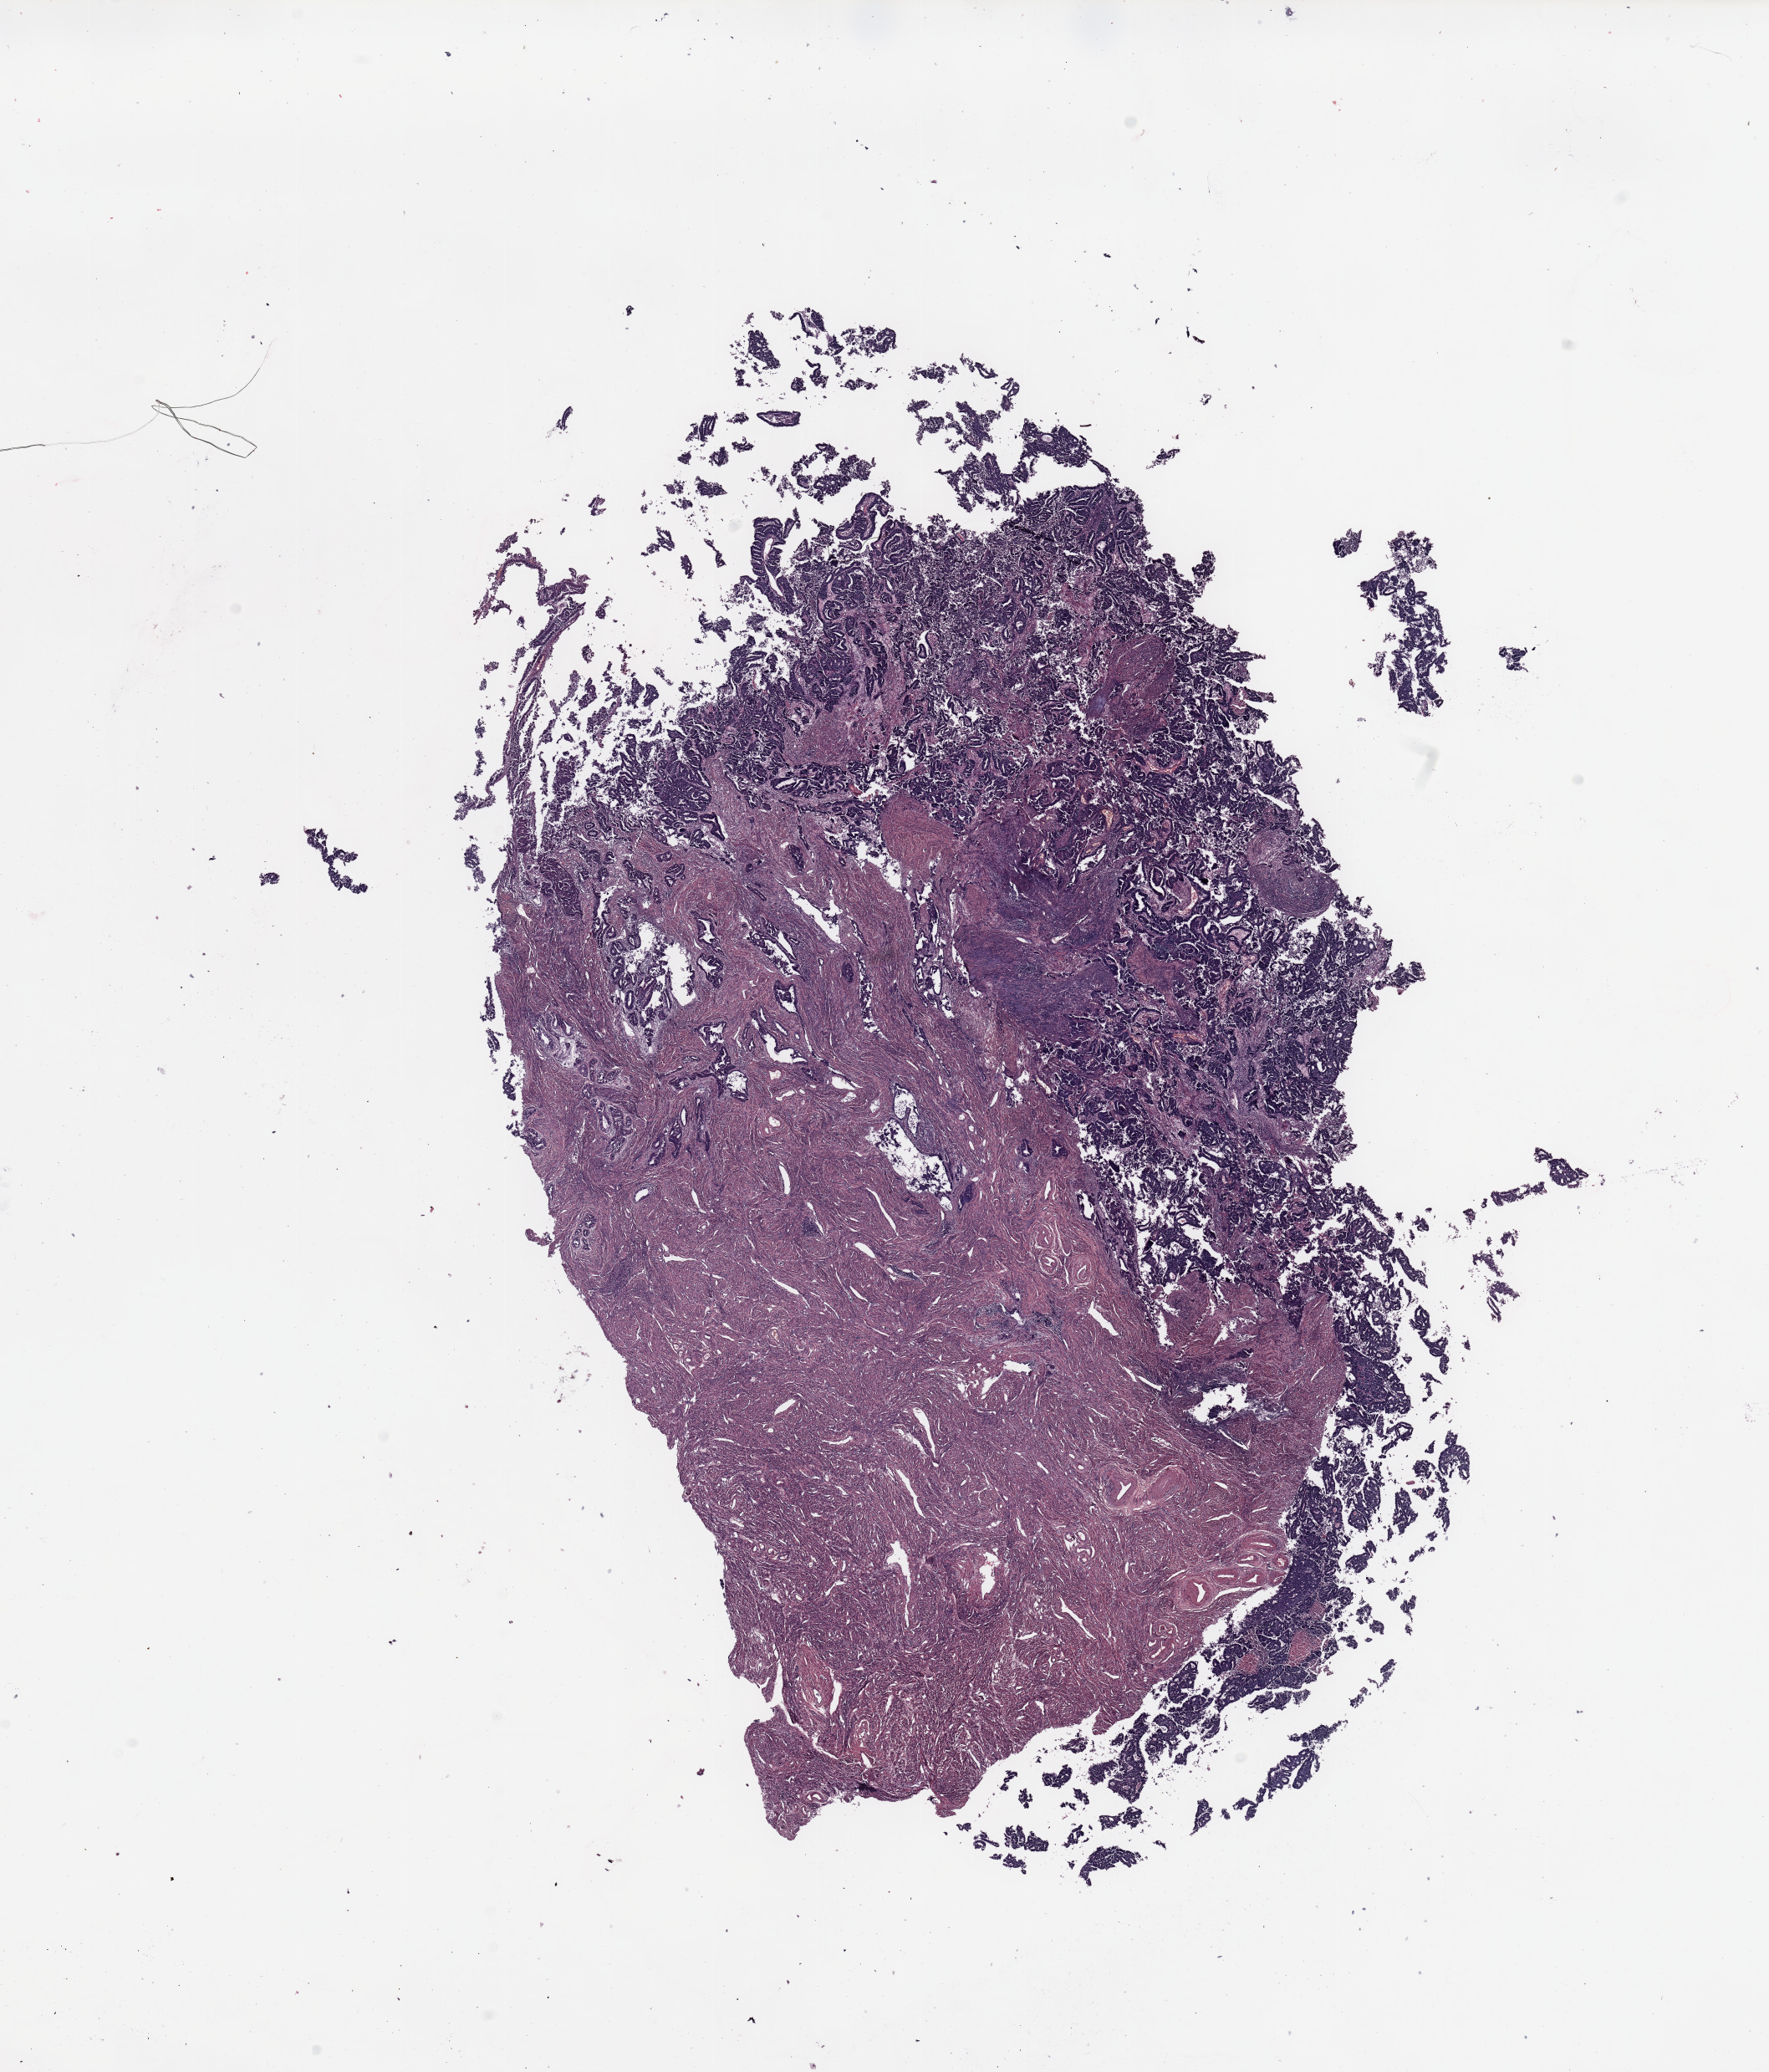
Digitized Hematoxylin and eosin (H&E) stained tissue section (whole slide) — a low-resolution overview of the entire scanned area, about 16.7 x 19.6 mm; tumour tissue sample, uterus. Female, 67 y/o. Histologic grade: G2 (moderately differentiated).
Diagnosis: Endometrioid adenocarcinoma, NOS. AJCC pathologic stage: I.